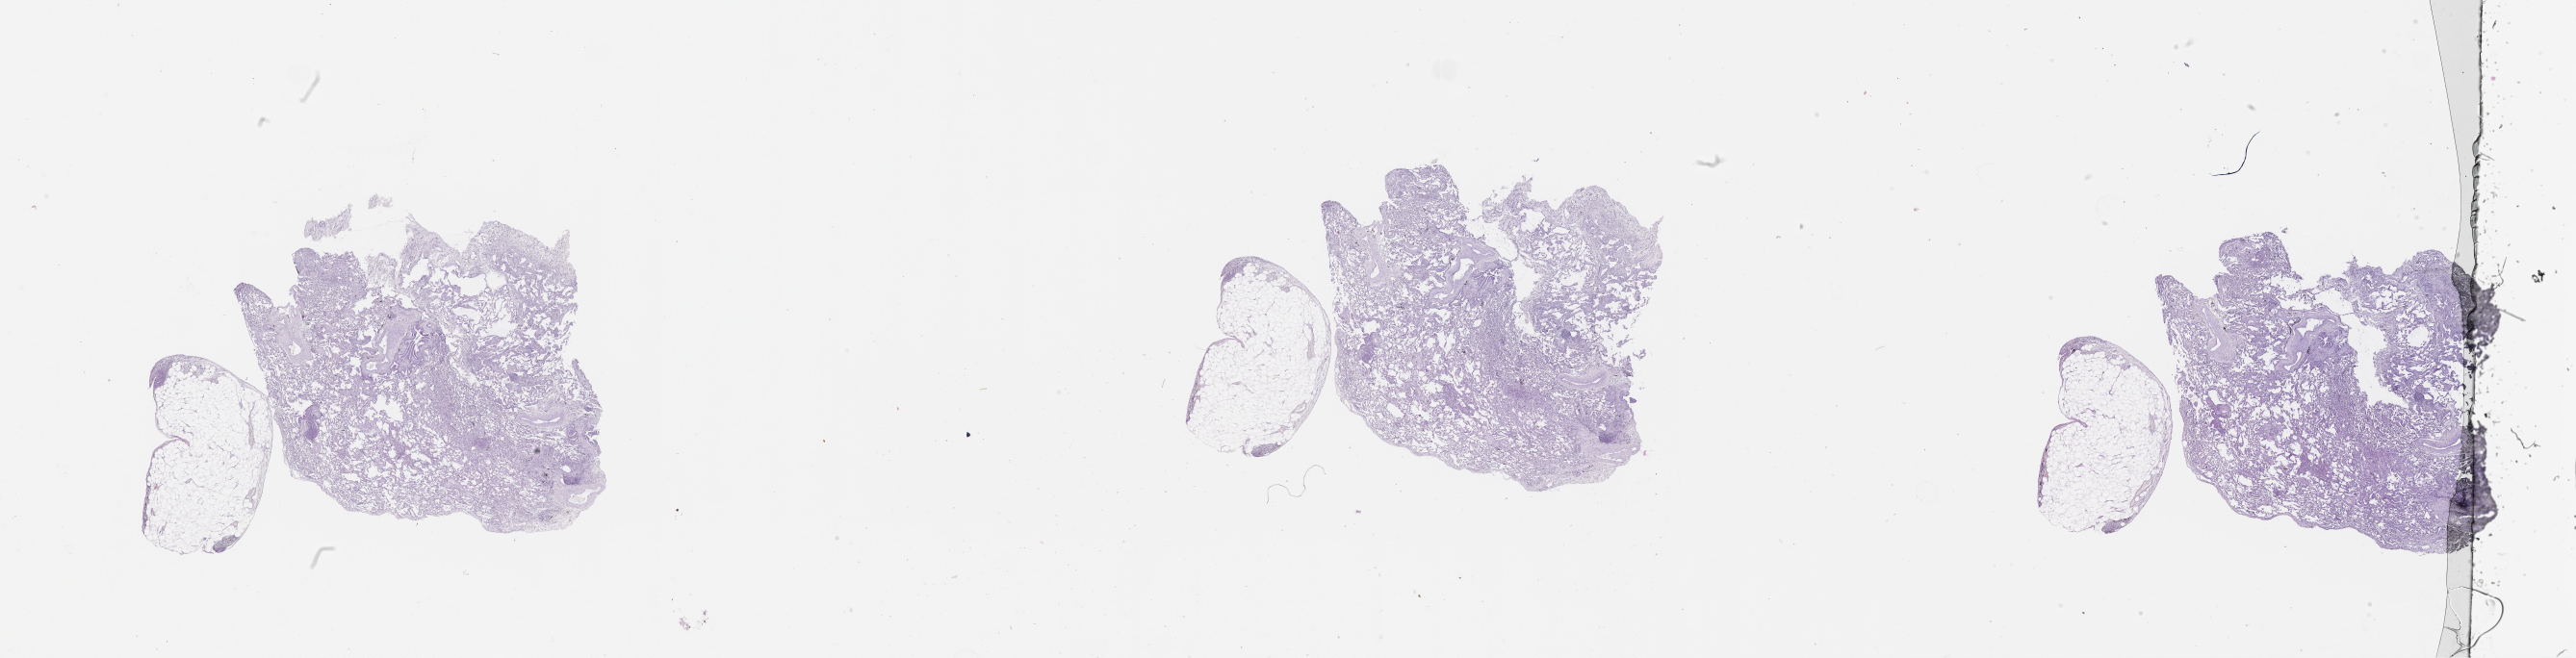
H&E whole-slide image — shown as a low-resolution overview of the whole scanned area (about 43.1 x 11.0 mm, acquisition: 20x scan), lung, normal (non-tumour) tissue. Male, 70 y/o.
This section: normal (non-tumour) tissue from the same patient. Patient diagnosis (cohort enrolment): squamous cell carcinoma (lung).